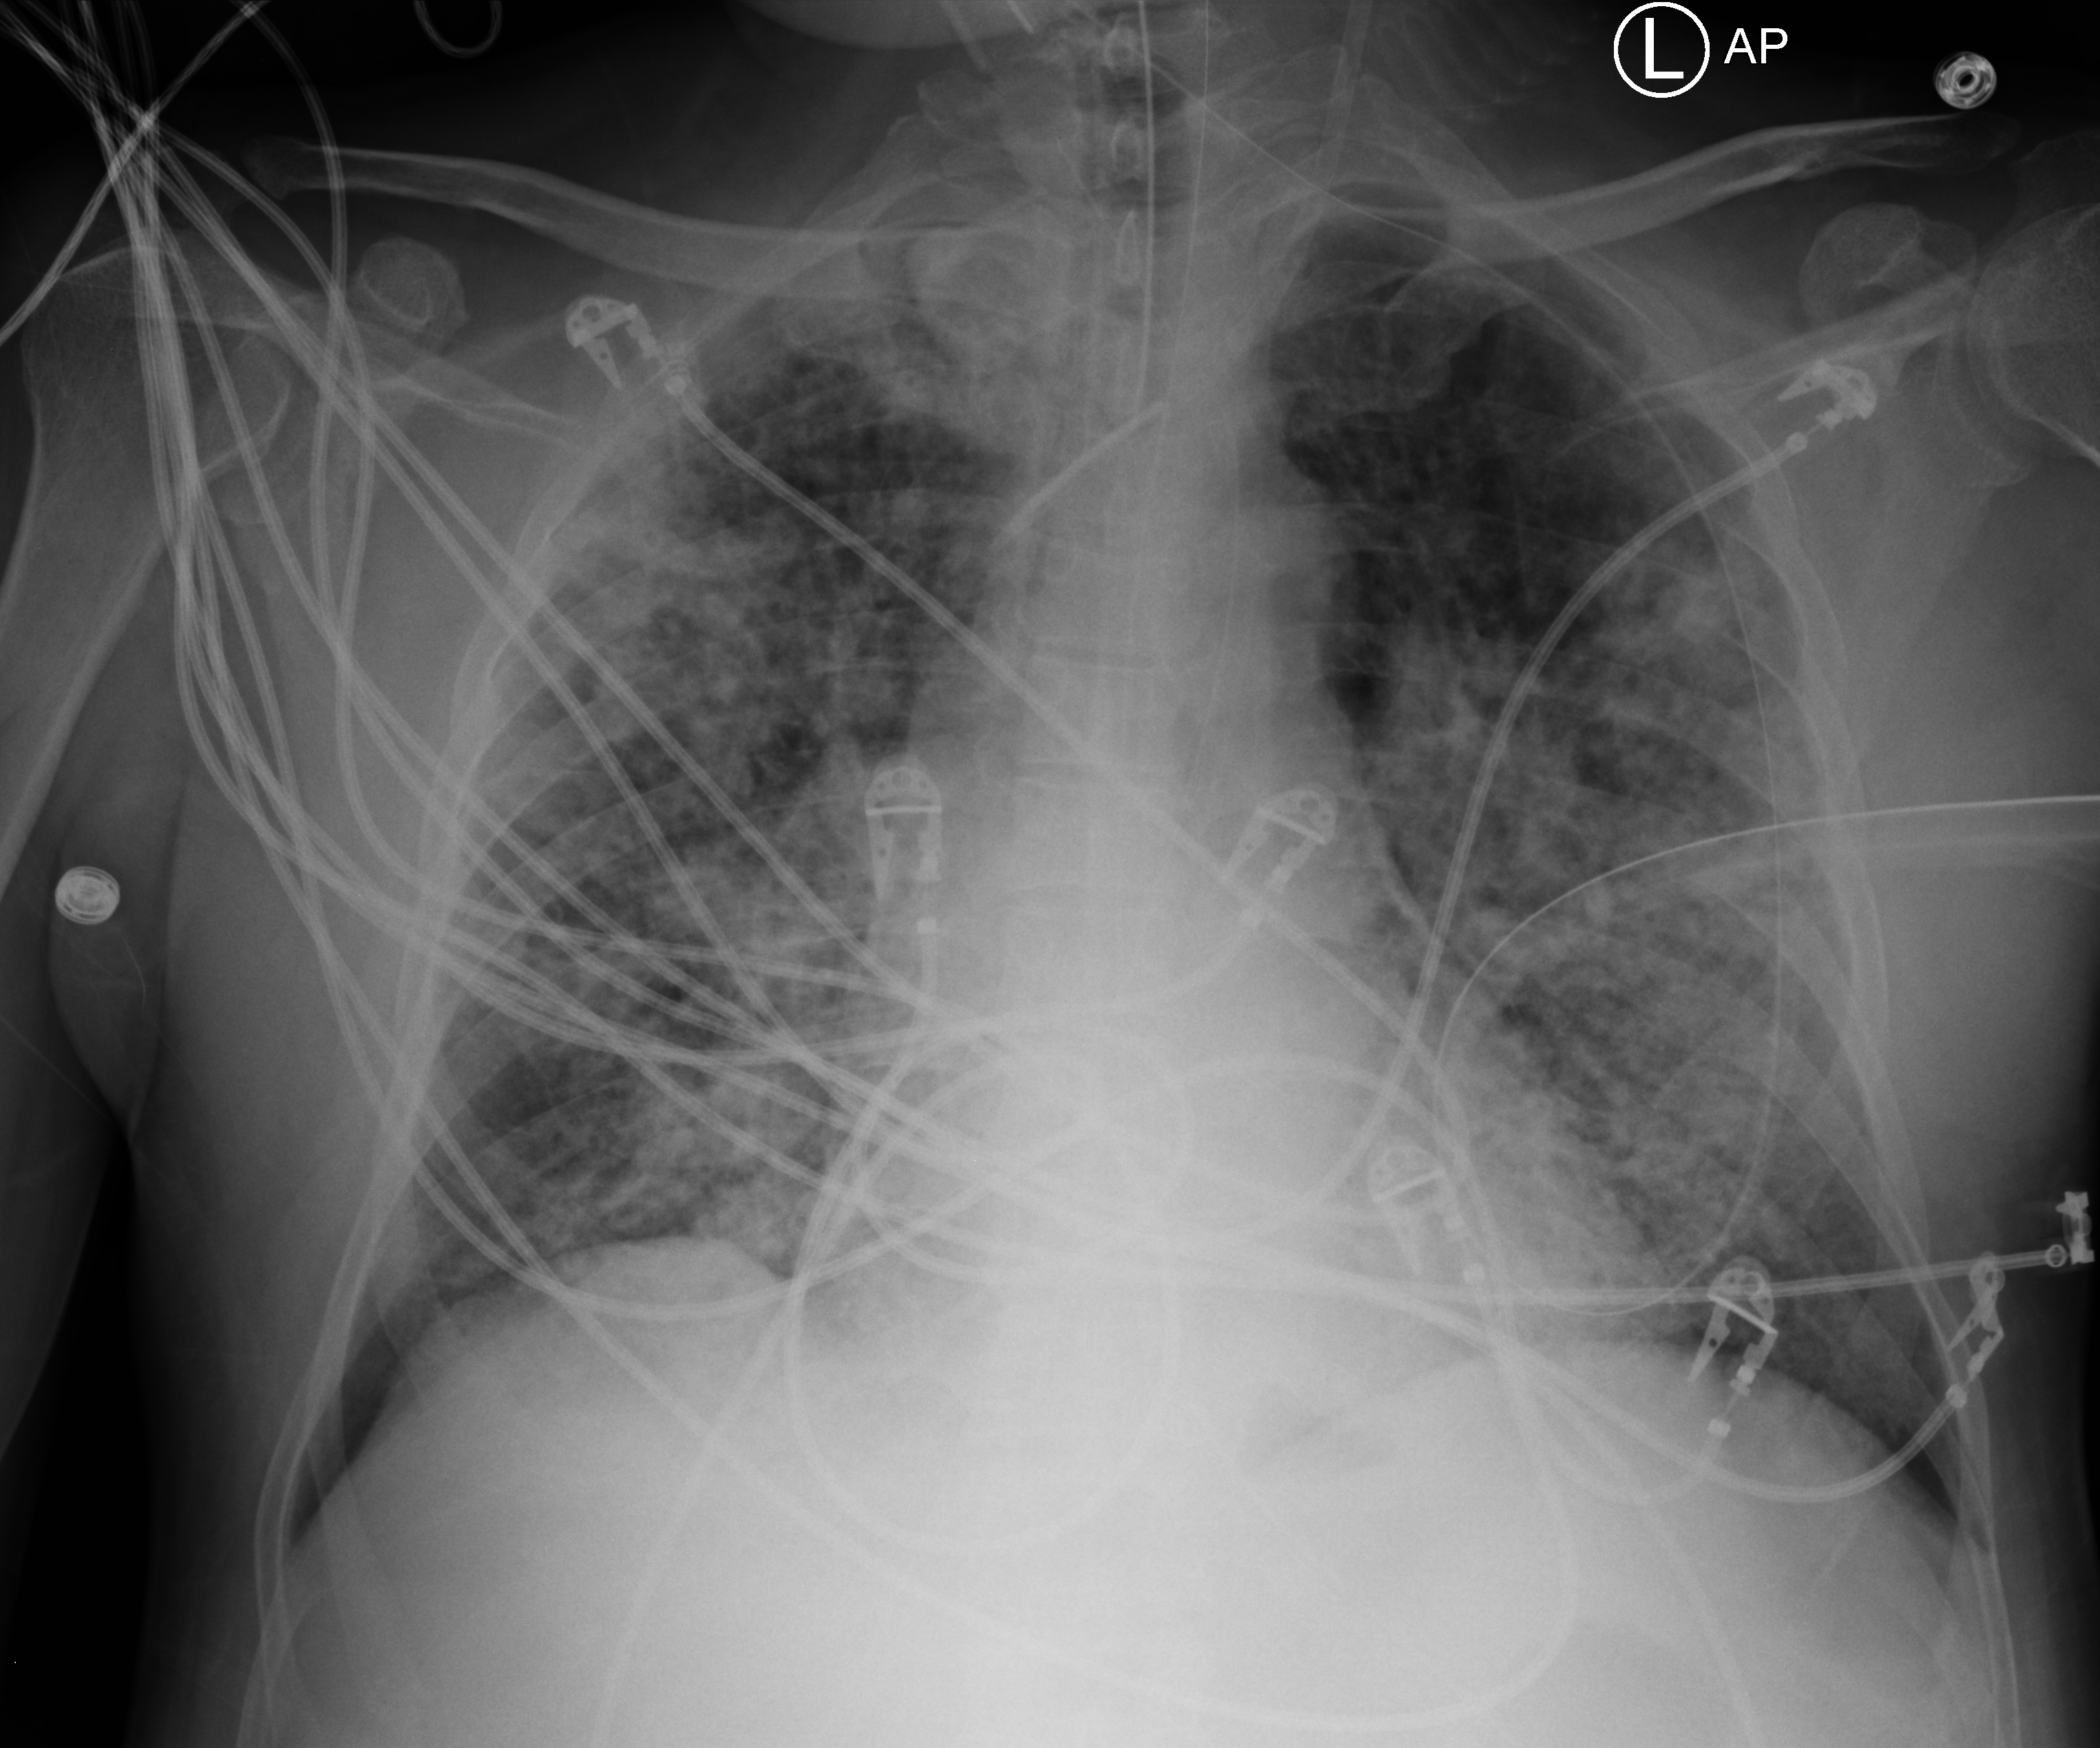
Chest X-ray (portable). Male patient hospitalised with COVID-19, age 60–74 years.
Admission-level facts for this patient (not findings on this image; timing relative to this image not recorded): admitted to intensive care during this hospital stay: yes.